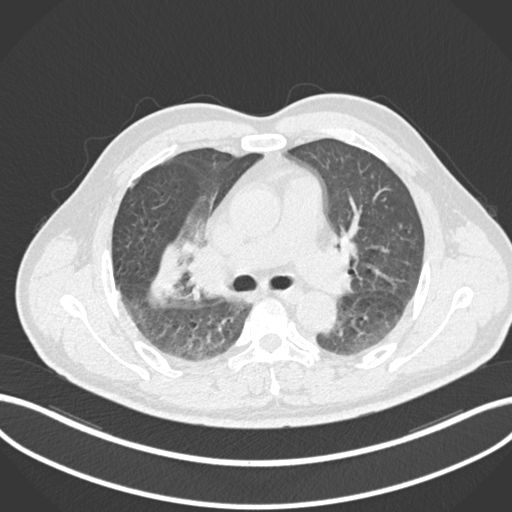
Chest CT, one axial slice; position 639 of 852 along the scan axis; reconstruction kernel B30f; lung window (W 1500 / L -600 HU); 1 mm slice thickness; 512 × 512 image matrix. Patient: male, 55 years. Case-level facts recorded for this patient, not image findings: clinical TNM (as recorded): T3 N2 M1.
Structures marked on this image (bounding box drawn by a radiologist):
- lung tumour (recorded histology: adenocarcinoma): bounding box <143,239,184,304> (left, top, right, bottom; pixels)